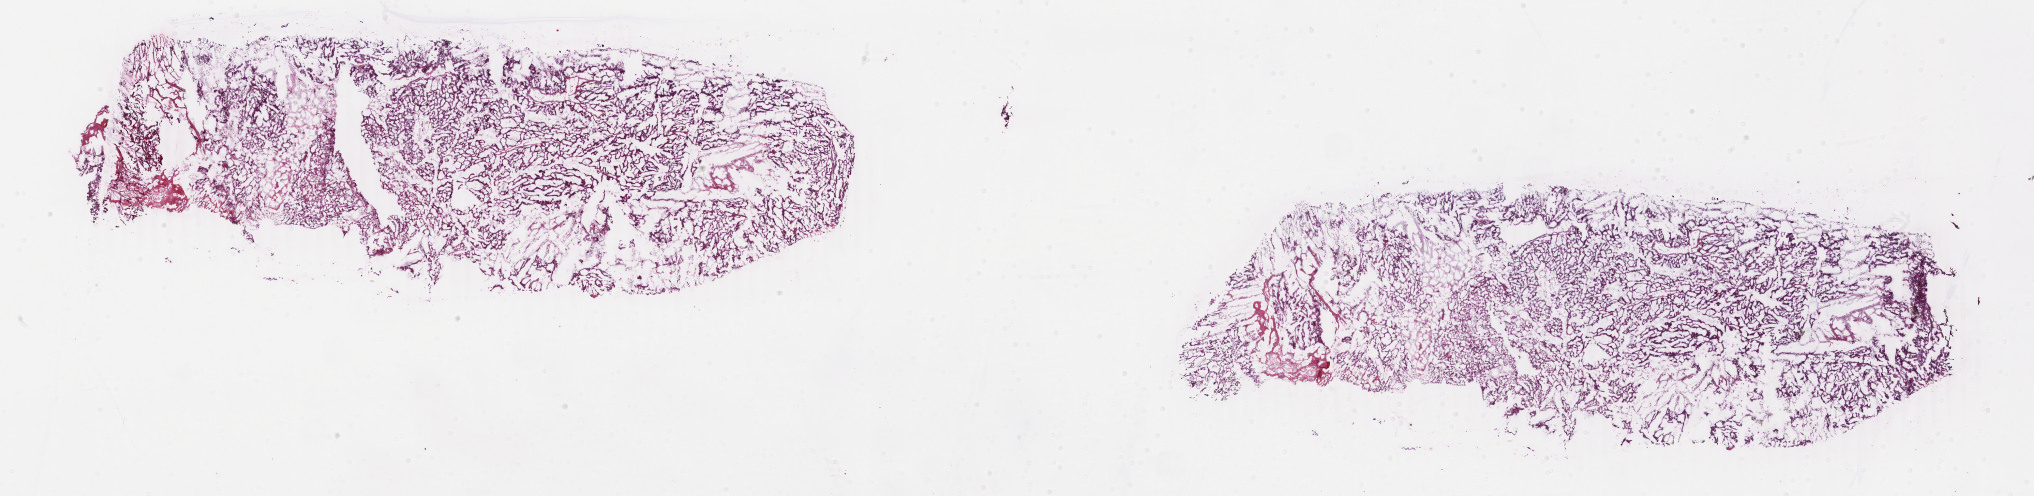
Whole-slide histology image, Hematoxylin and eosin (H&E) stained, low-resolution overview of the scanned area, about 32.4 x 7.9 mm (from a 40x scan). Frozen section from the bottom of the tissue portion. Primary tumour sample from the uterus. Female patient; age at initial diagnosis 77 years.
Diagnosis: Endometrioid adenocarcinoma, NOS (endometrium).